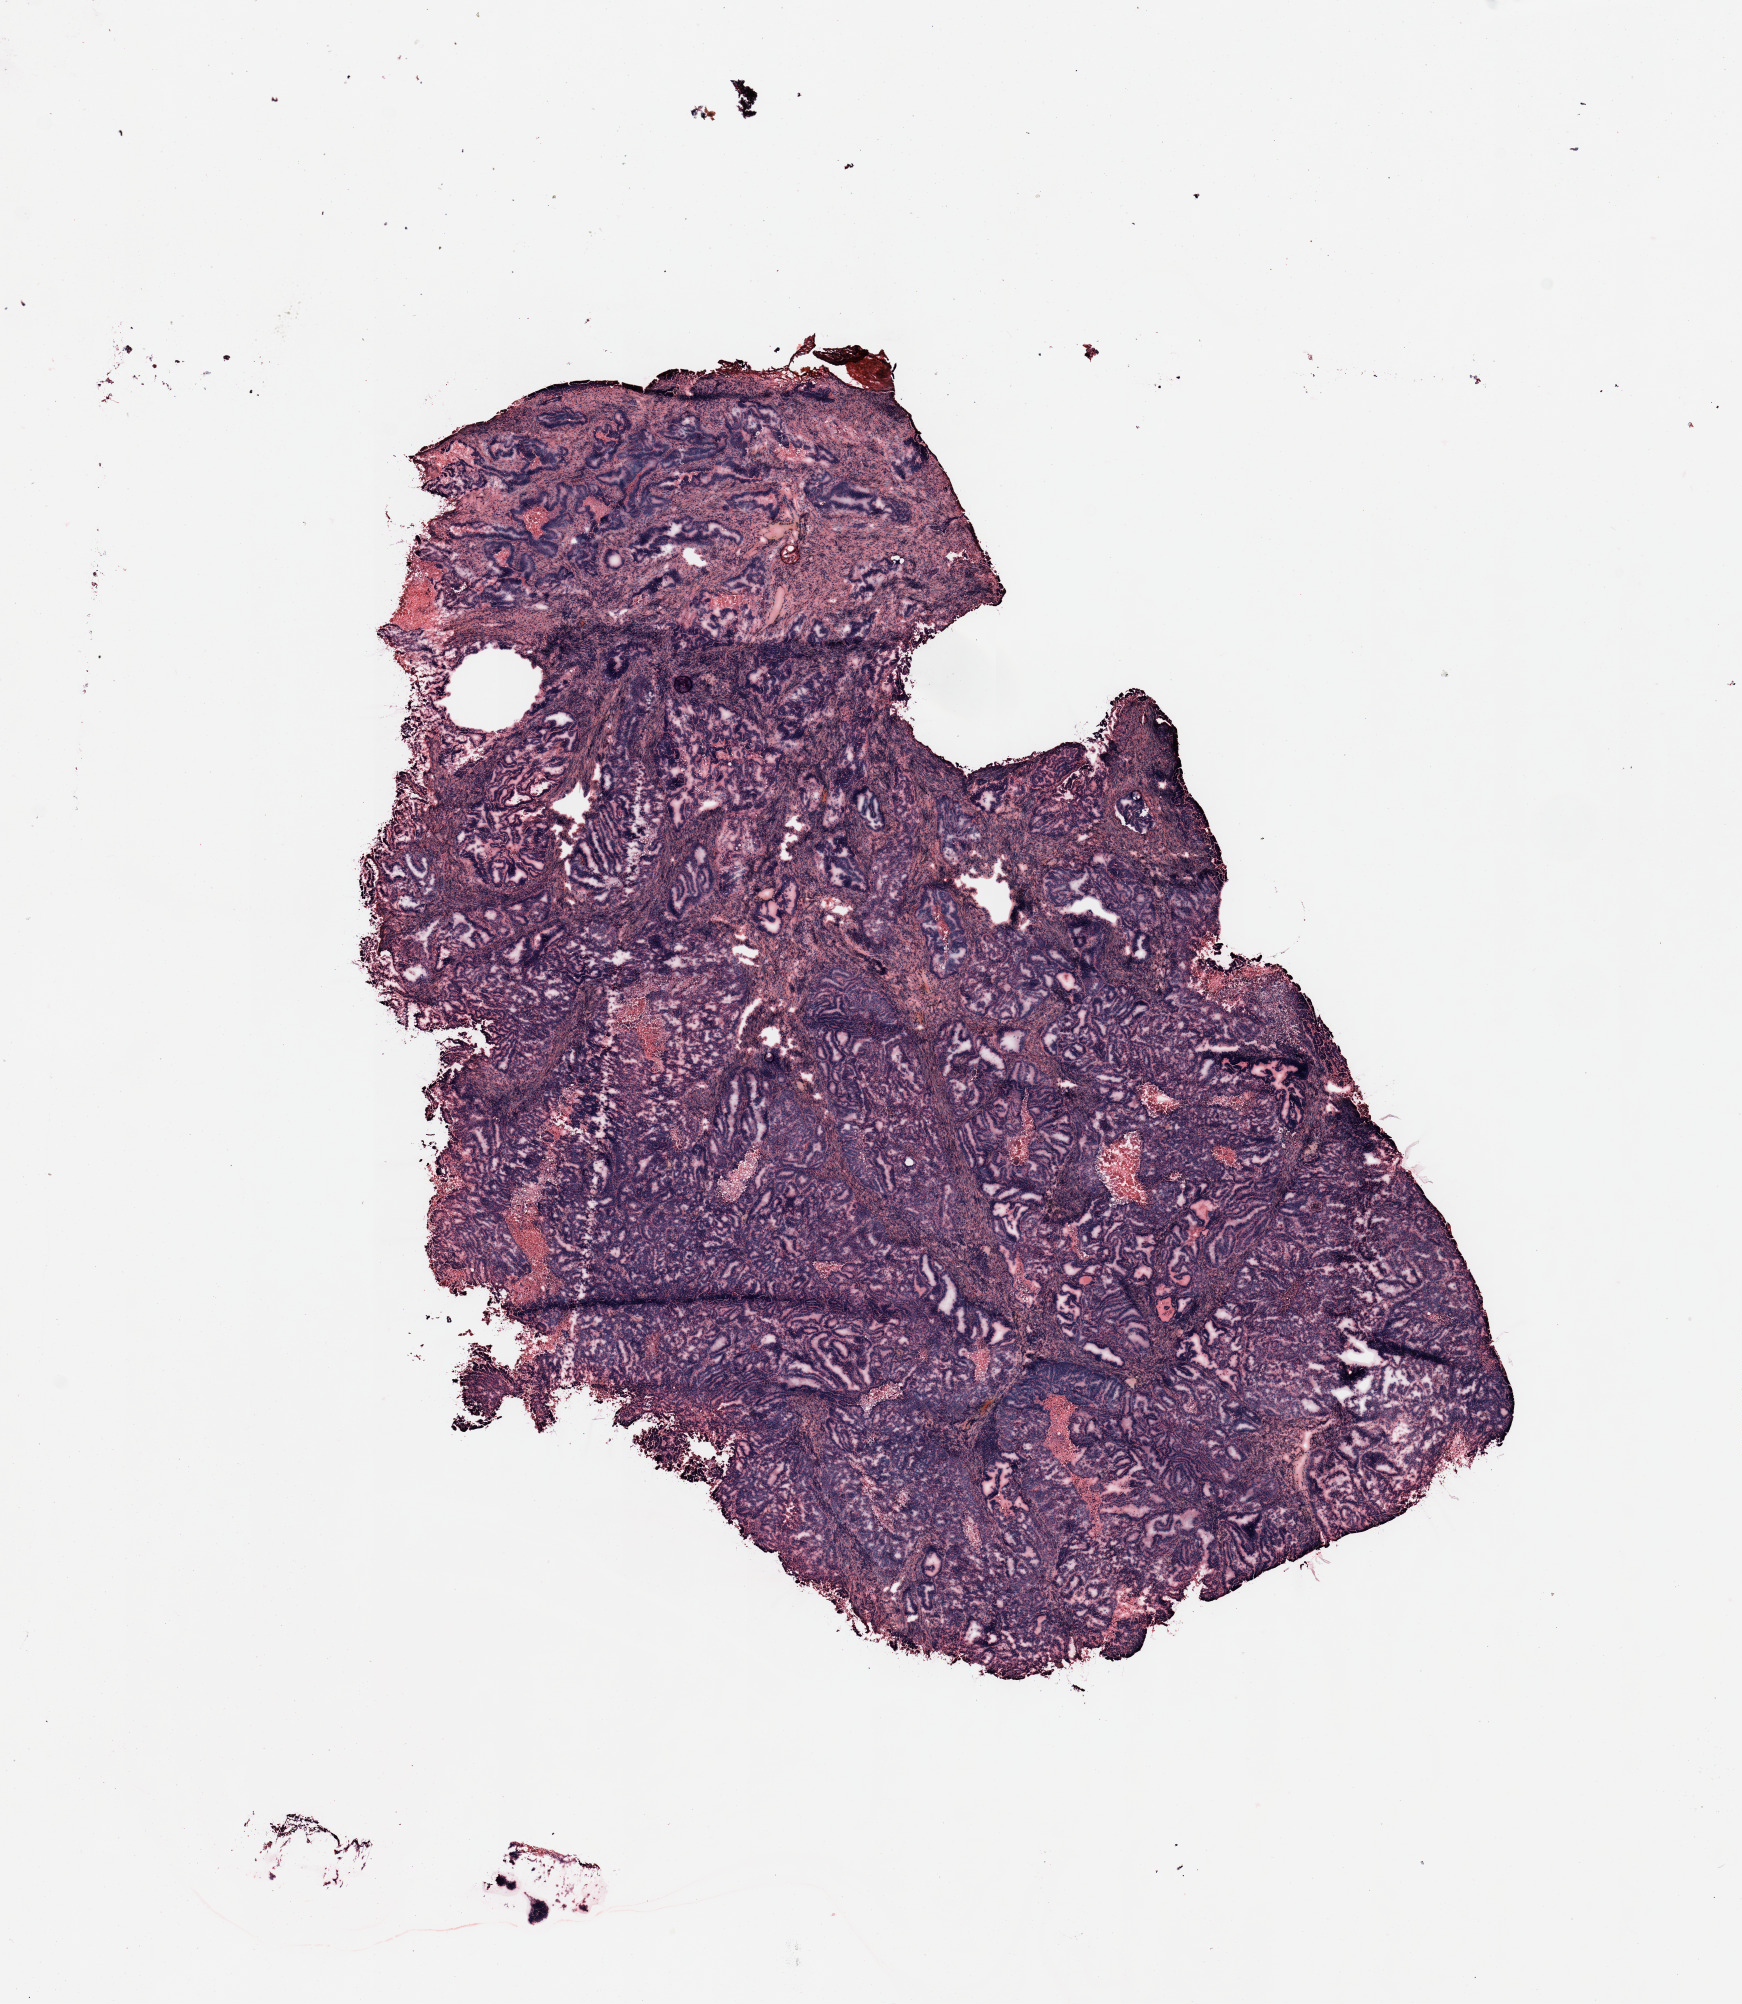
Whole-slide histology image, H&E — low-resolution overview of the scanned area, about 13.8 x 15.9 mm (from a 20x scan). Tumour tissue sample, sampled site: uterus. Female, 78 y/o. Histologic grade: G2 (moderately differentiated). Composition of this section per pathologist review: tumour nuclei 90%, necrosis 5%.
AJCC pathologic stage: I. Diagnosis: Endometrioid adenocarcinoma, NOS.